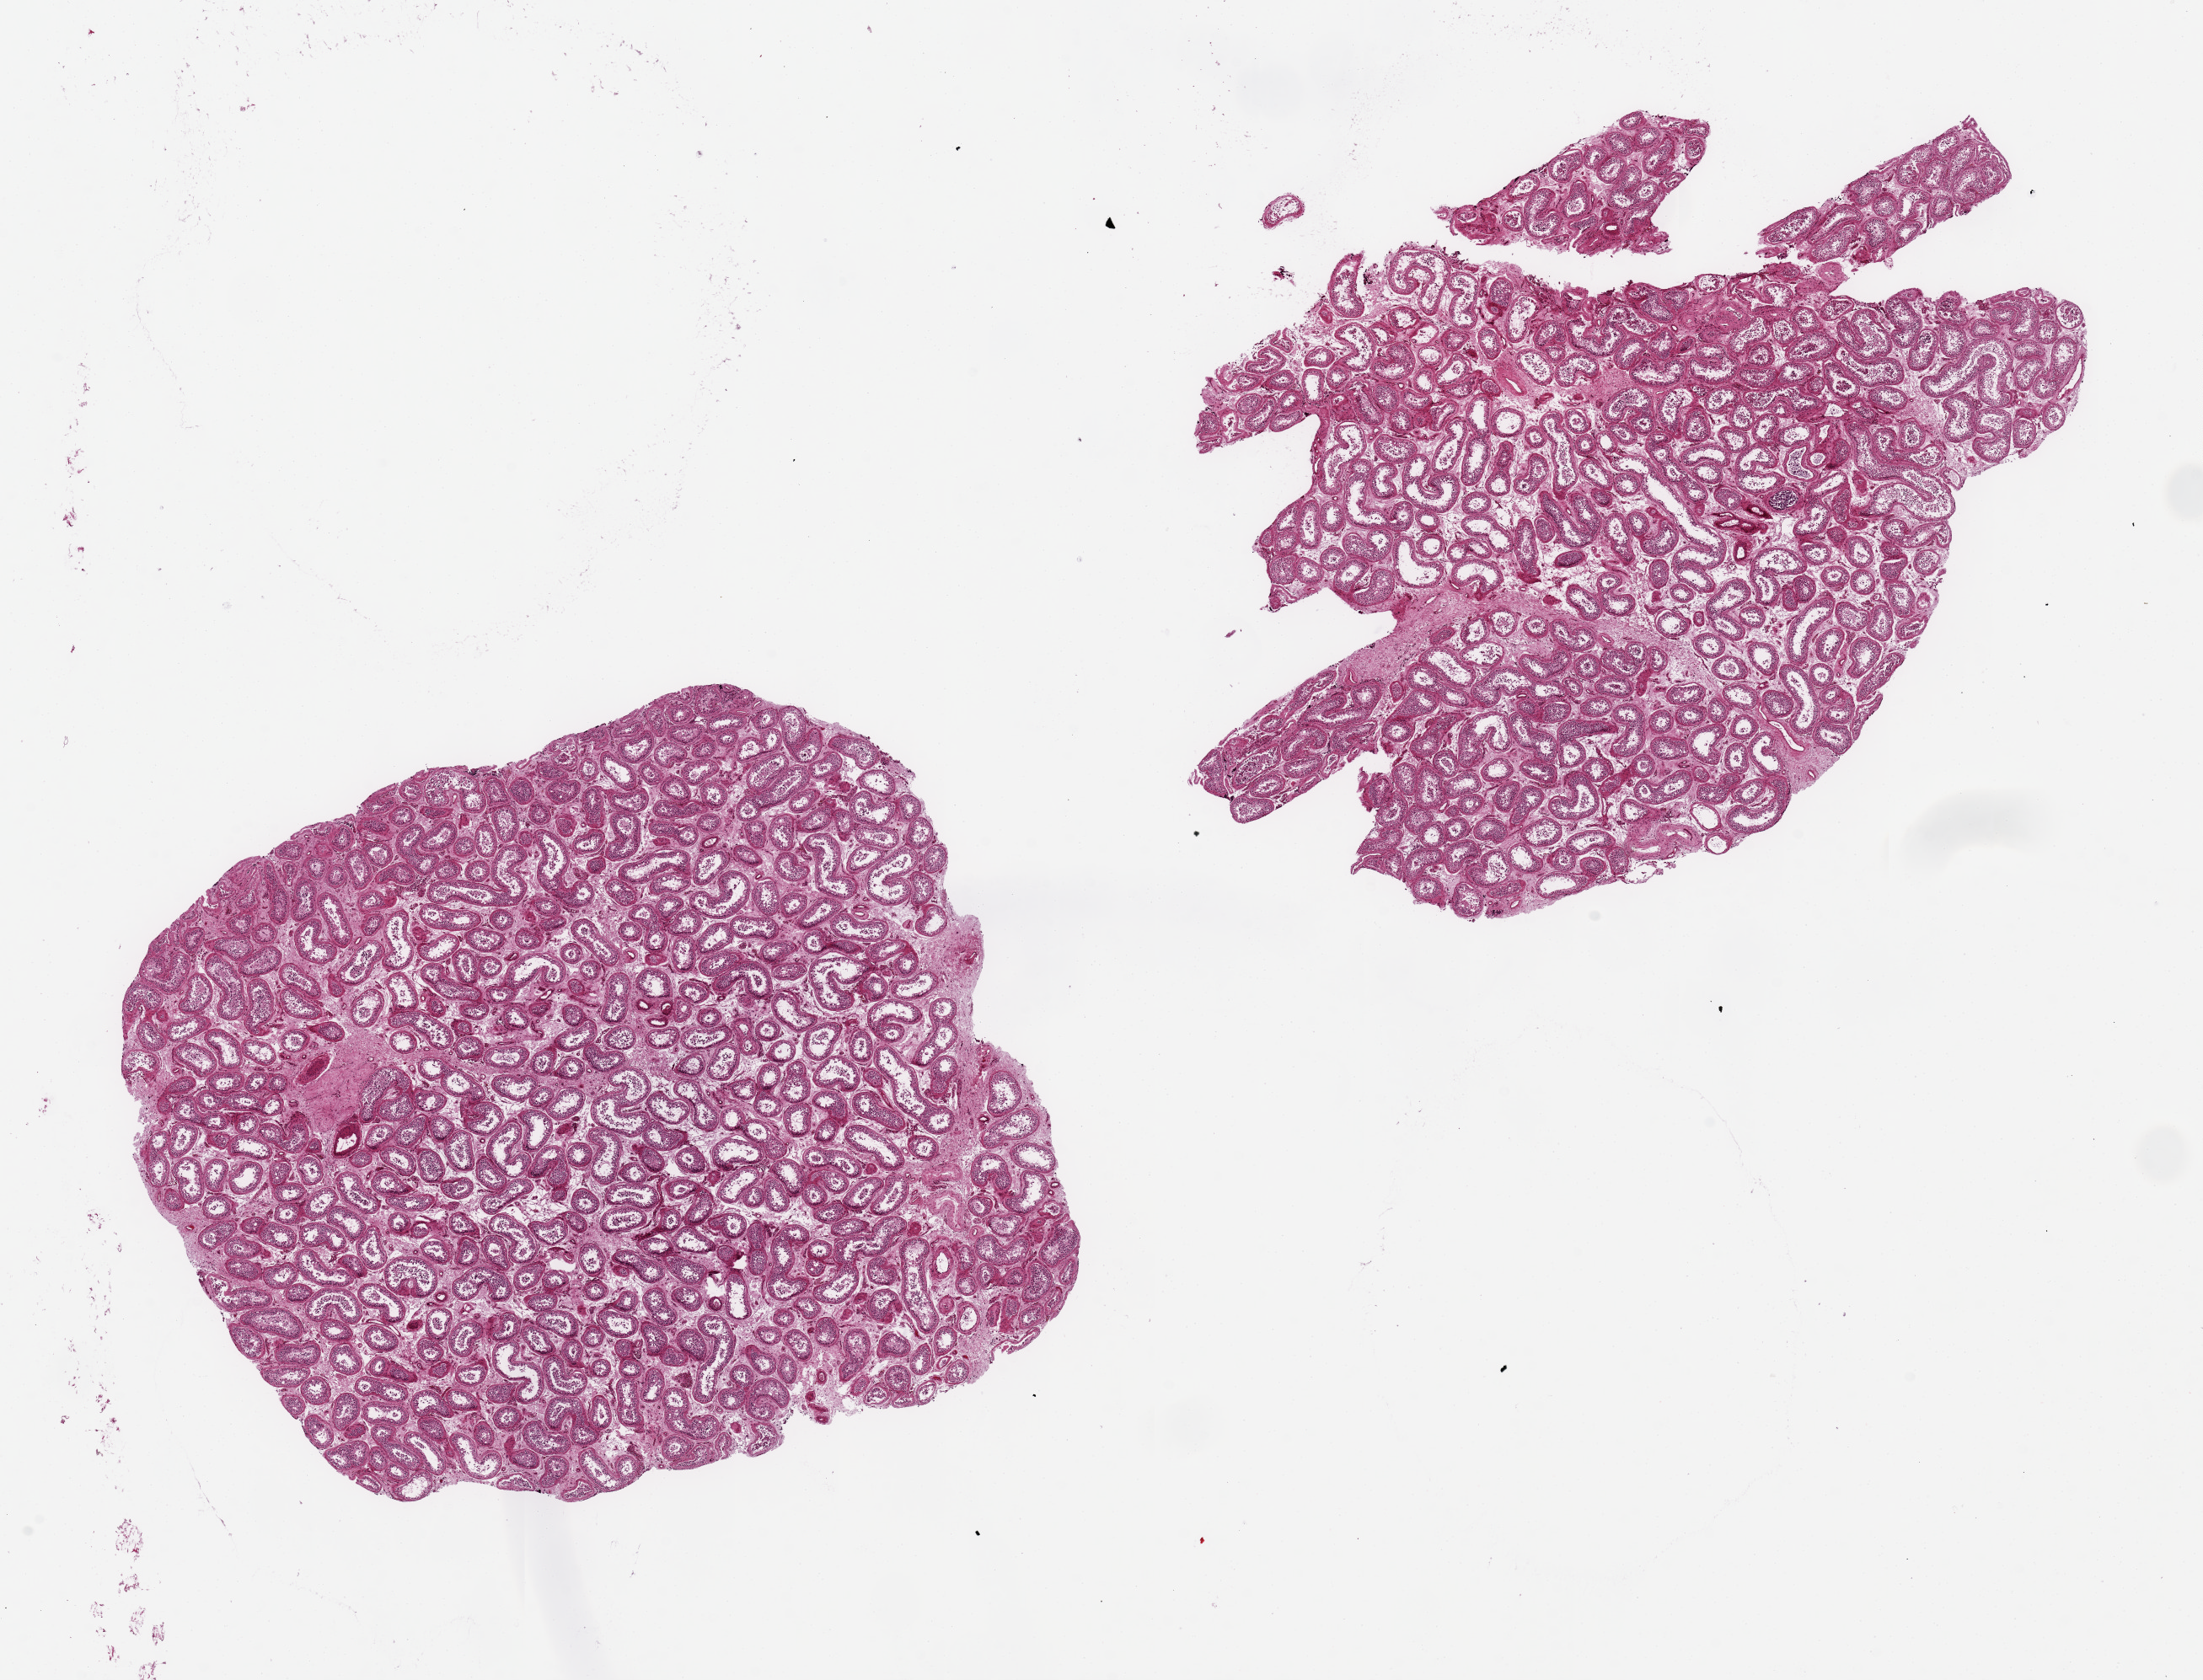
Whole-slide image, H&E stain, shown as a low-resolution overview of the whole scanned area (about 20.7 x 15.8 mm, acquisition: 20x scan). PAXgene-fixed paraffin-embedded (PFPE) section. Target tissue: testis. Tissue donor sample.
Review note (as recorded): 2 pieces 8x7 & 8x6 mm; moderately reduced spermatogenesis.